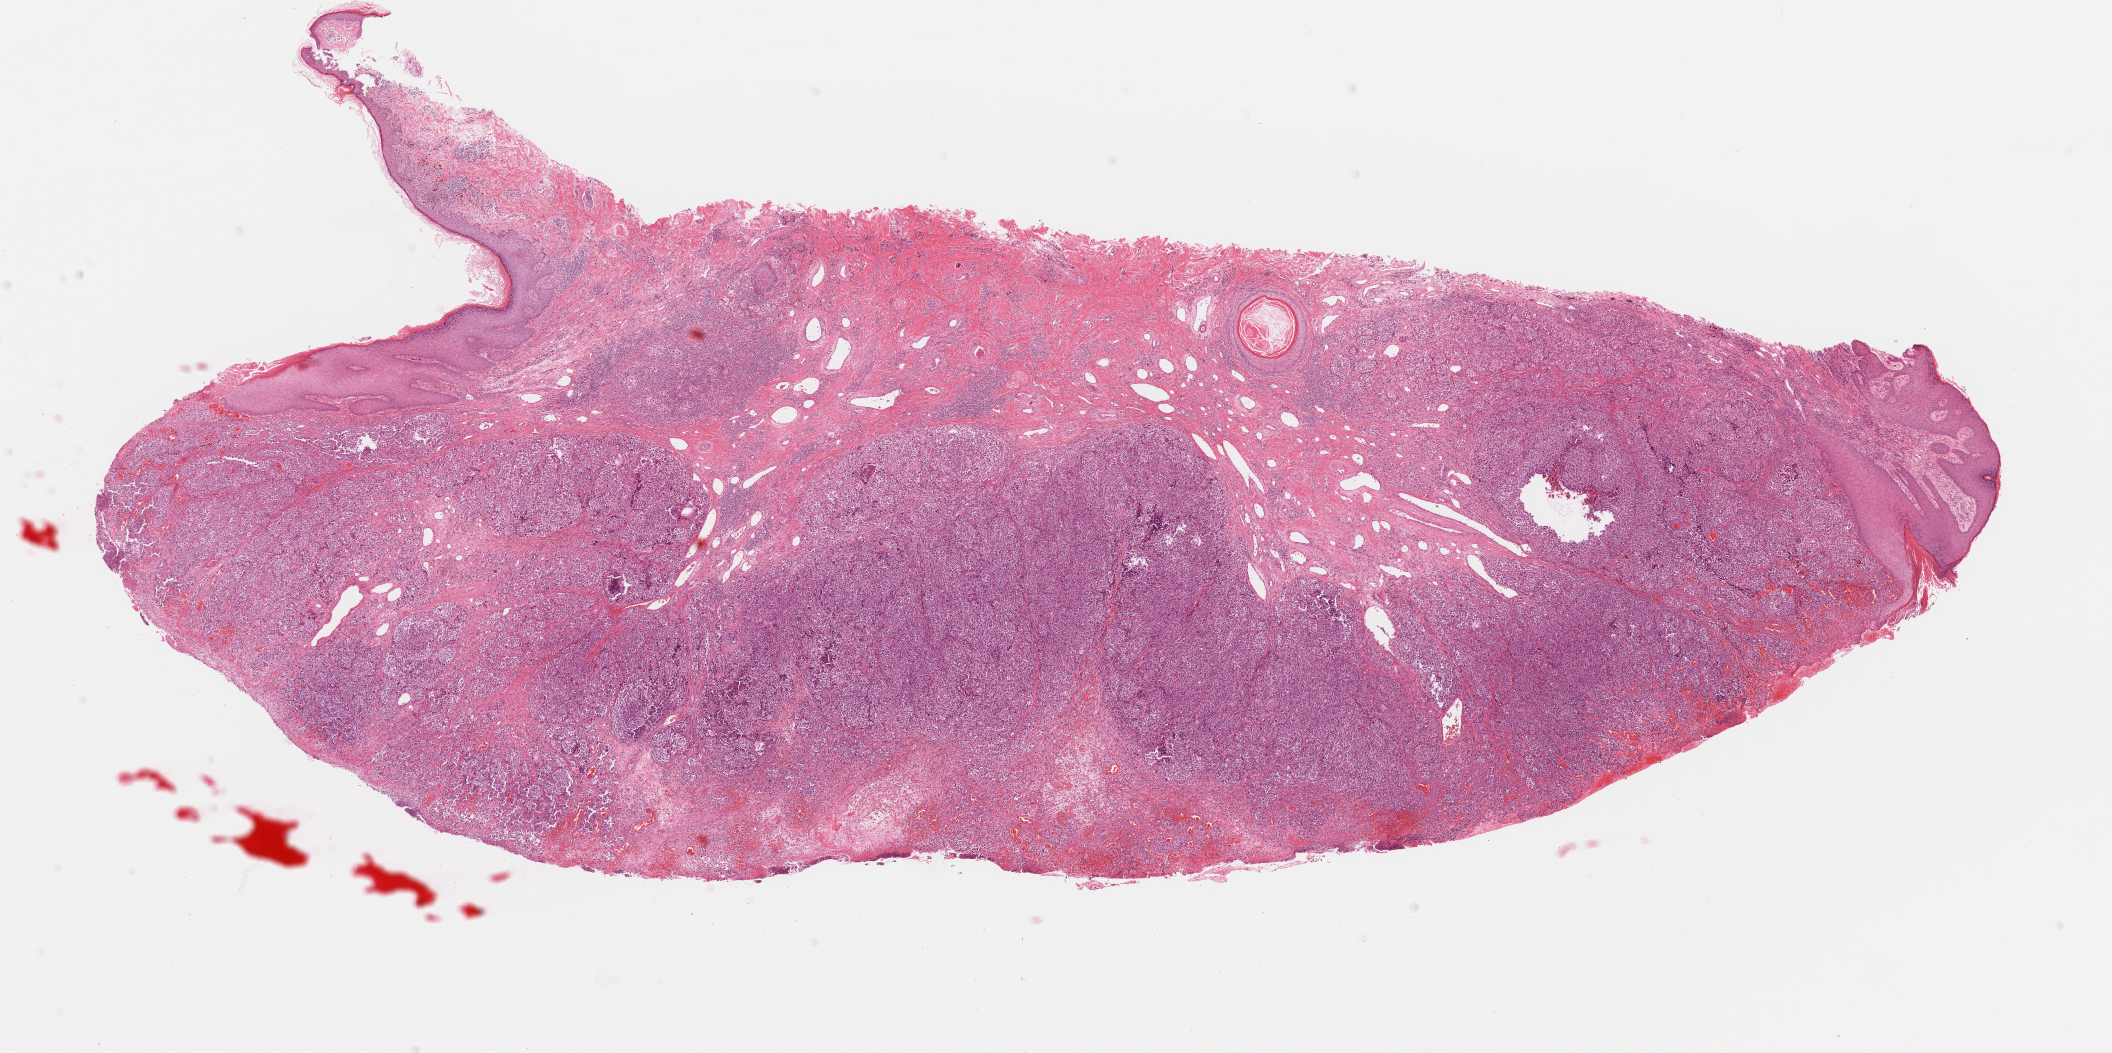
H&E whole-slide image — a low-resolution overview of the entire scanned area, about 16.7 x 8.3 mm (slide scanned at 40x). Formalin-fixed paraffin-embedded (FFPE) diagnostic section. Sample: primary tumour, skin. Patient: male, age at initial diagnosis 74 years.
- AJCC pathologic stage: IIC (7th edition)
- diagnosis: Malignant melanoma, NOS
- TNM: T4b N0 M0